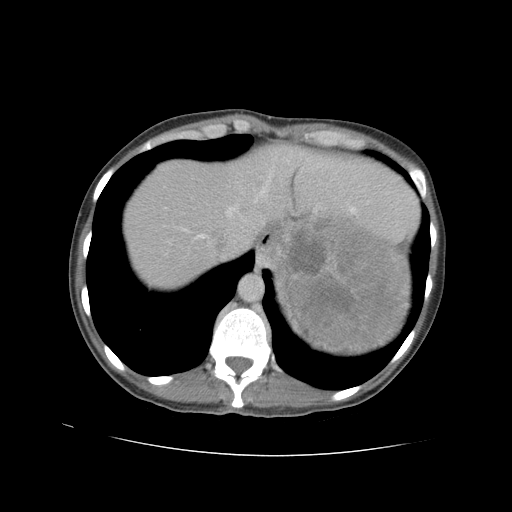
Contrast-enhanced abdominal CT, one axial slice. Position 79 of 90 along the scan axis. Intravenous contrast given. Soft-tissue window (W 400 / L 40 HU). 512 × 512 image matrix, field of view 360 × 360 mm. Female patient. From the clinical record (not read from this slice): diagnosis: adrenocortical carcinoma; tumour side: left adrenal; tumour size at pathology: 18 cm.
Structures marked on this image (semi-automatic segmentation, software-assisted and operator-edited):
- mass: bounding box [x1, y1, x2, y2] px = [280, 222, 406, 350]